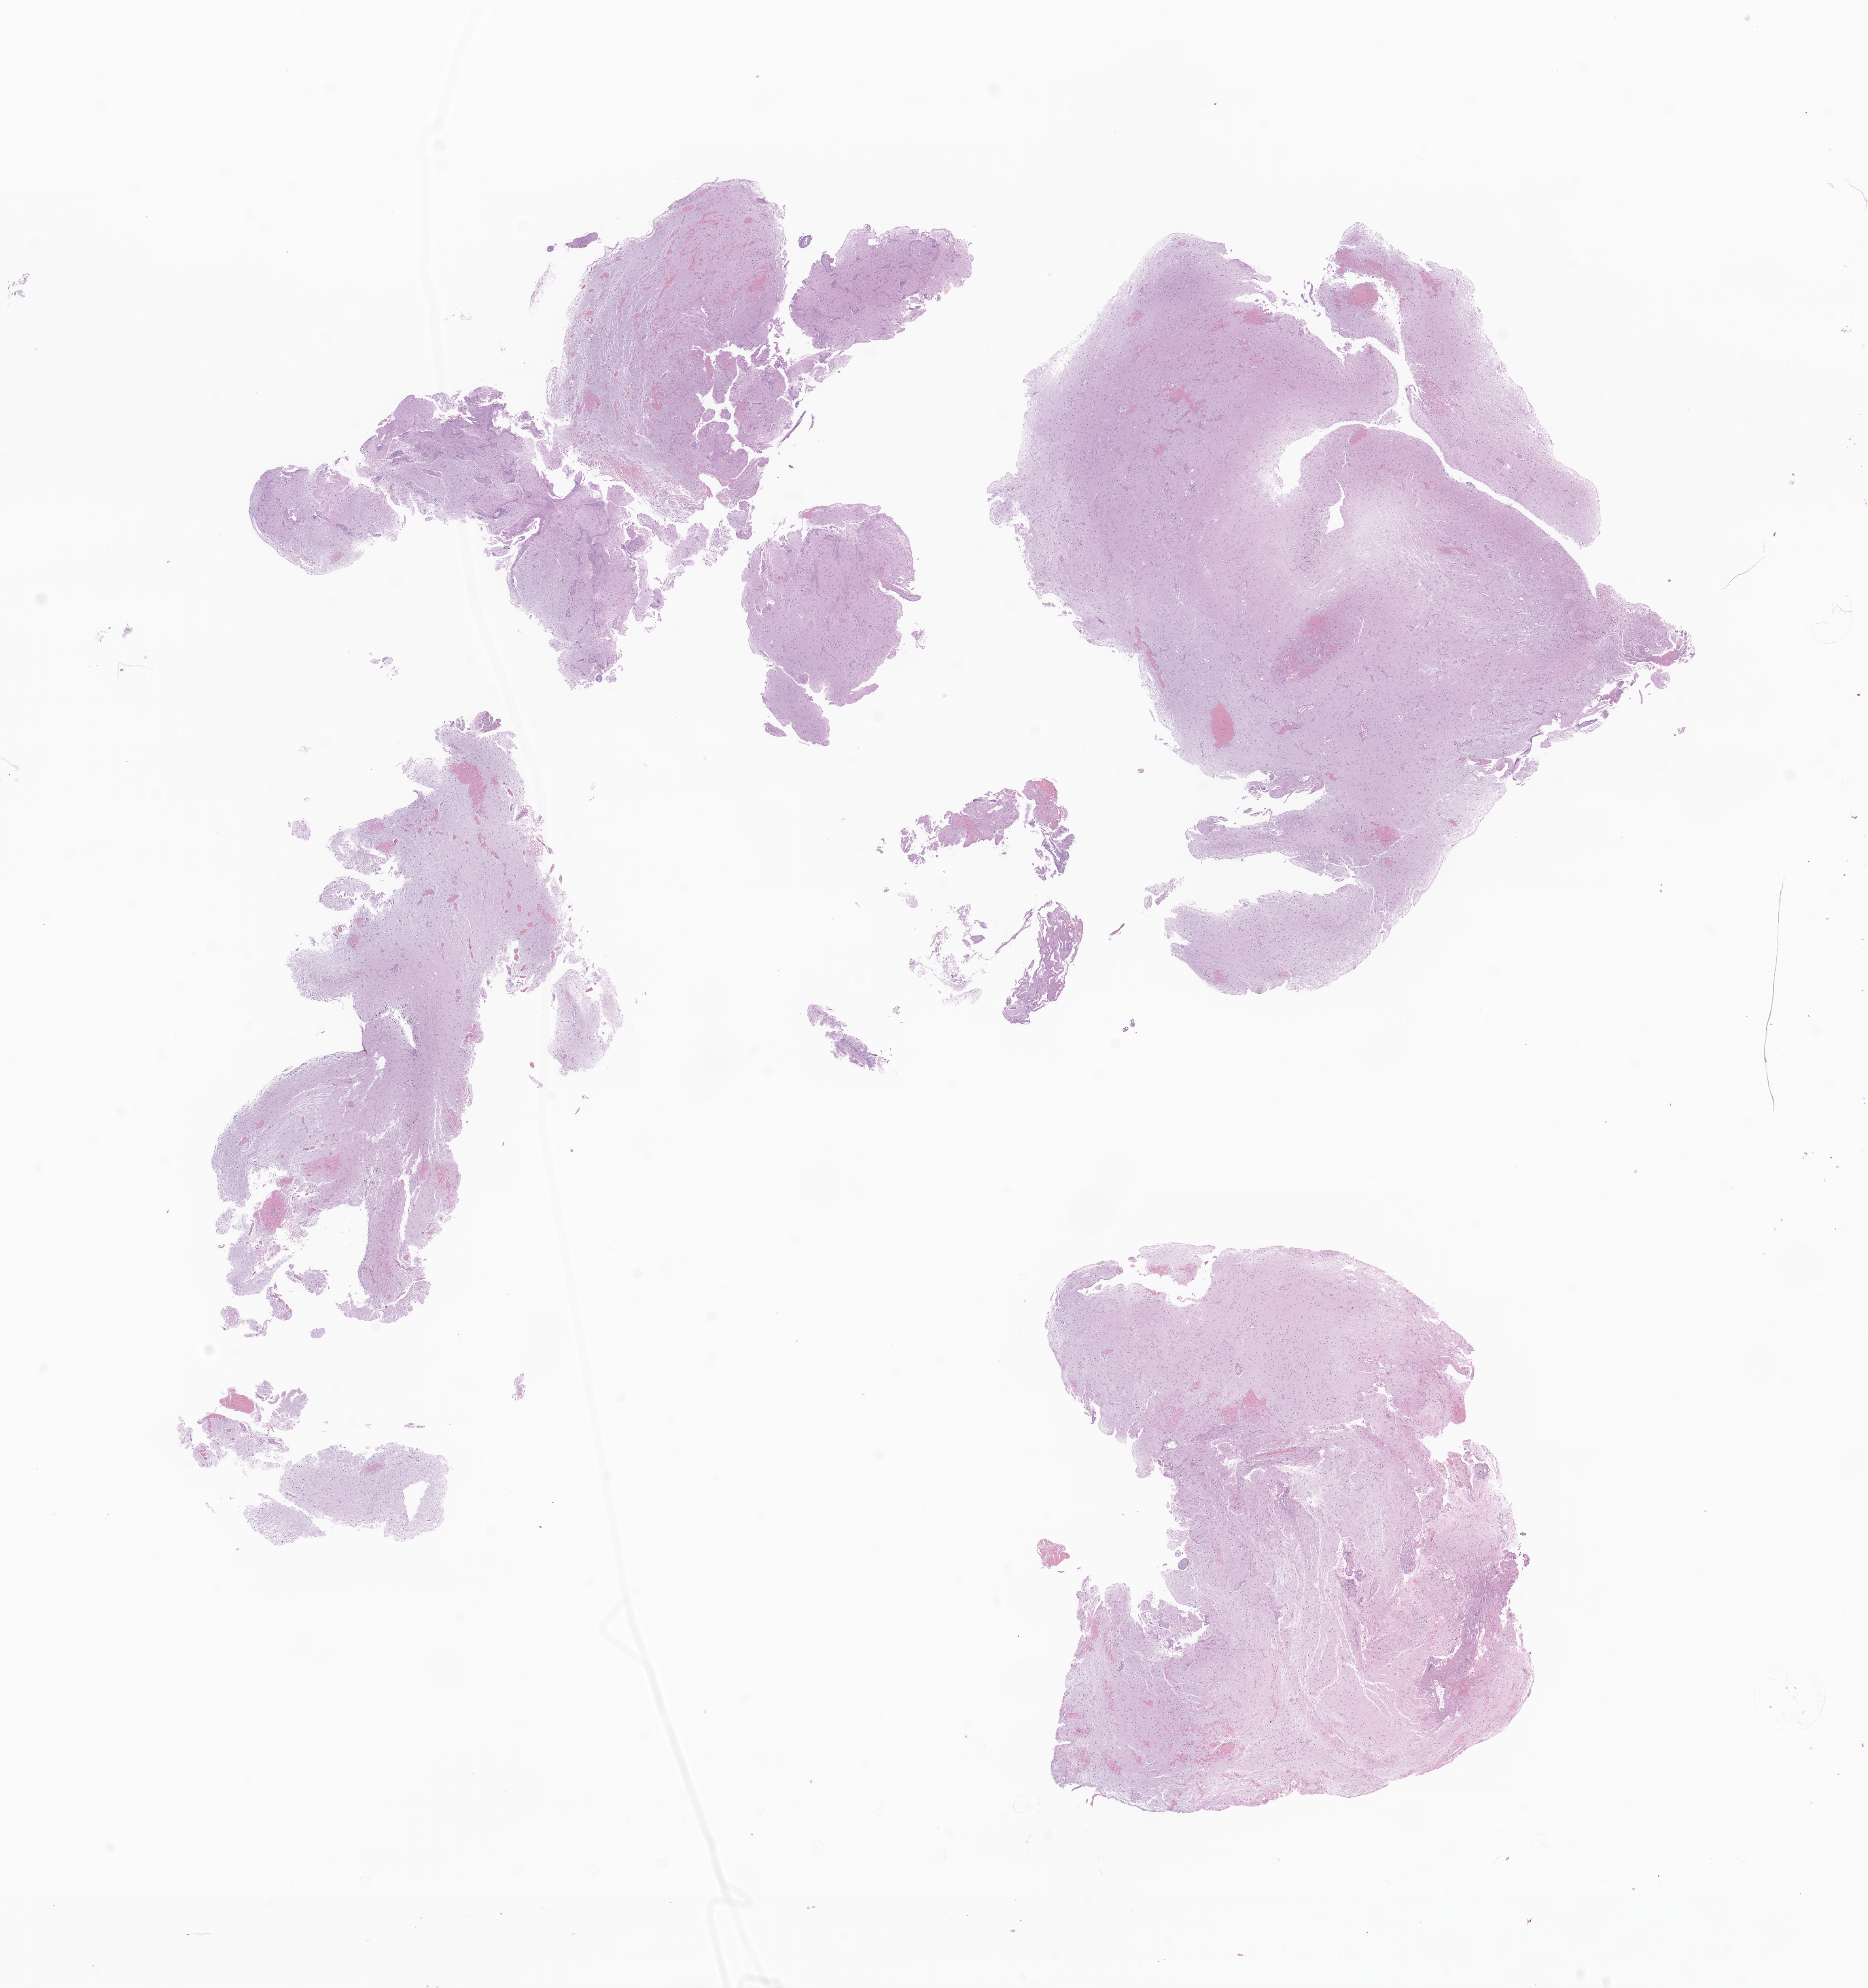
Digitized haematoxylin and eosin-stained section of tumor tissue from the cerebellum, a low-resolution overview of the entire scanned area, about 19.9 x 21.2 mm; formalin-fixed, paraffin-embedded (FFPE) tissue. Patient female; age 165 months (13 years 9 months).
Diagnosis: Pilocytic astrocytoma.